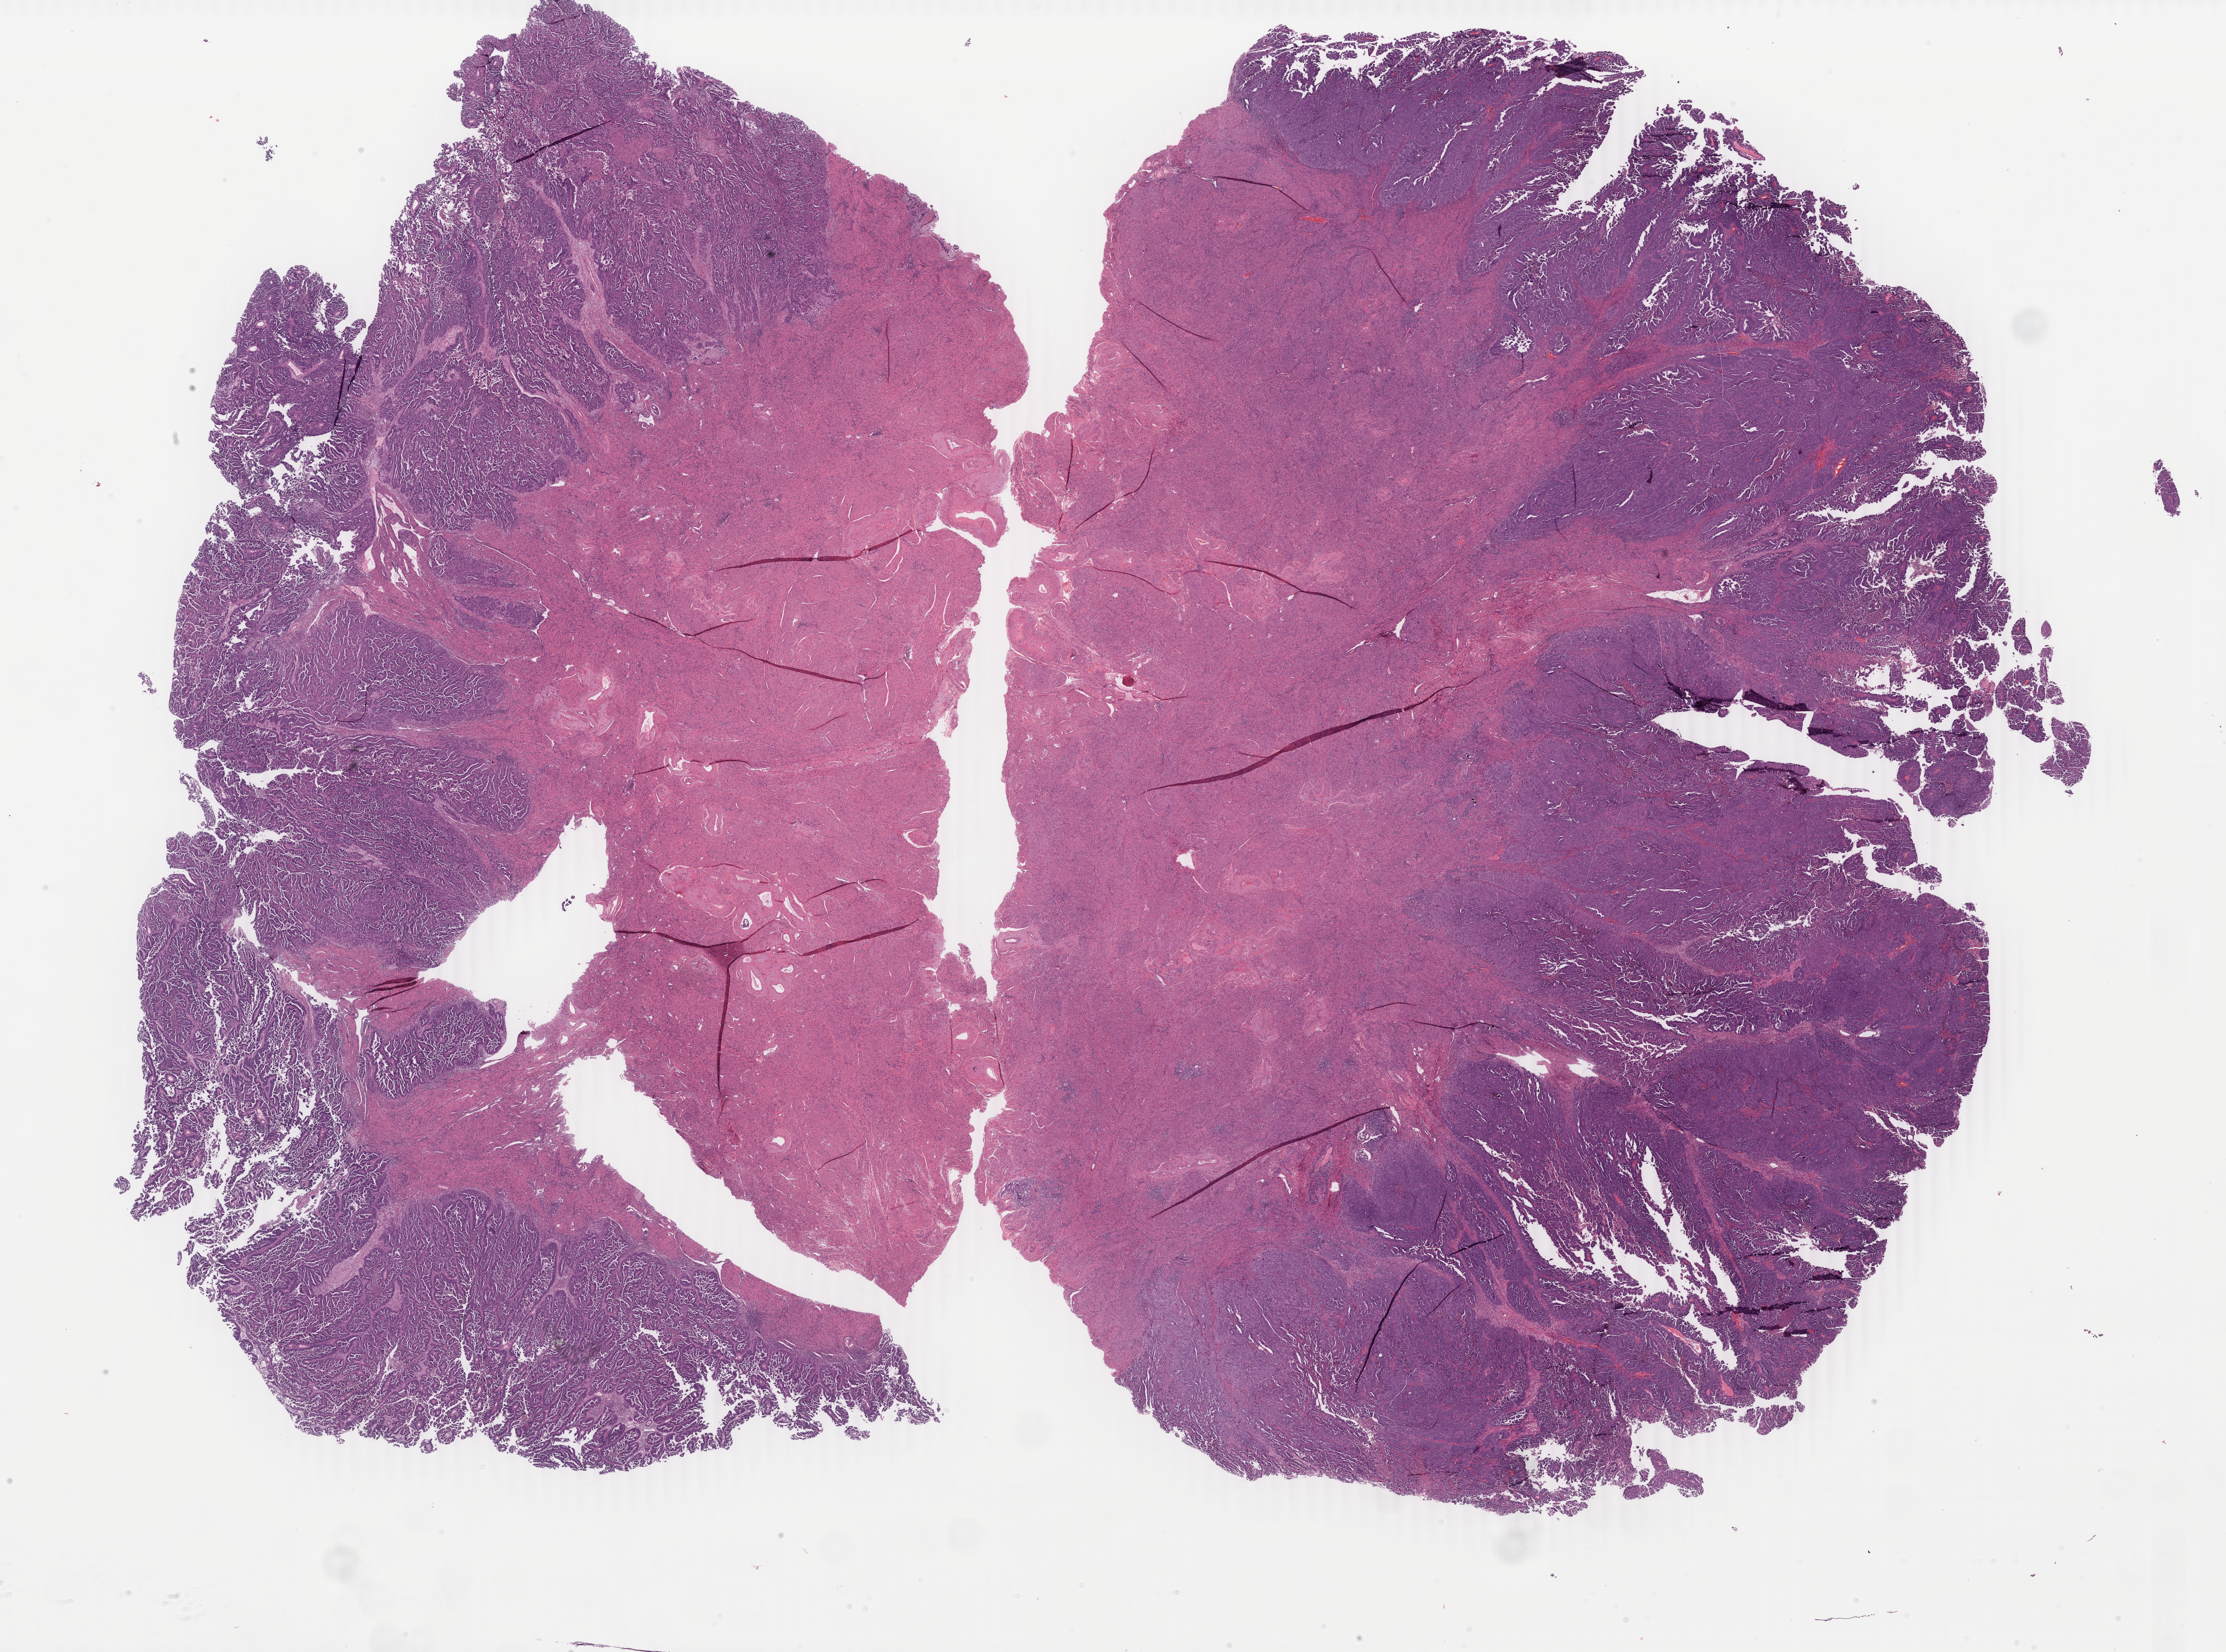
H&E whole-slide image — a low-resolution overview of the entire scanned area, about 30.5 x 22.6 mm; formalin-fixed paraffin-embedded (FFPE) diagnostic section; uterus, primary tumour sample. Patient: female, age at initial diagnosis 76 years. Histologic grade: high grade.
Pathologic diagnosis: Serous cystadenocarcinoma, NOS (endometrium). Lymph nodes positive (case pathology): 2 of 21 examined. FIGO stage: IIIC.